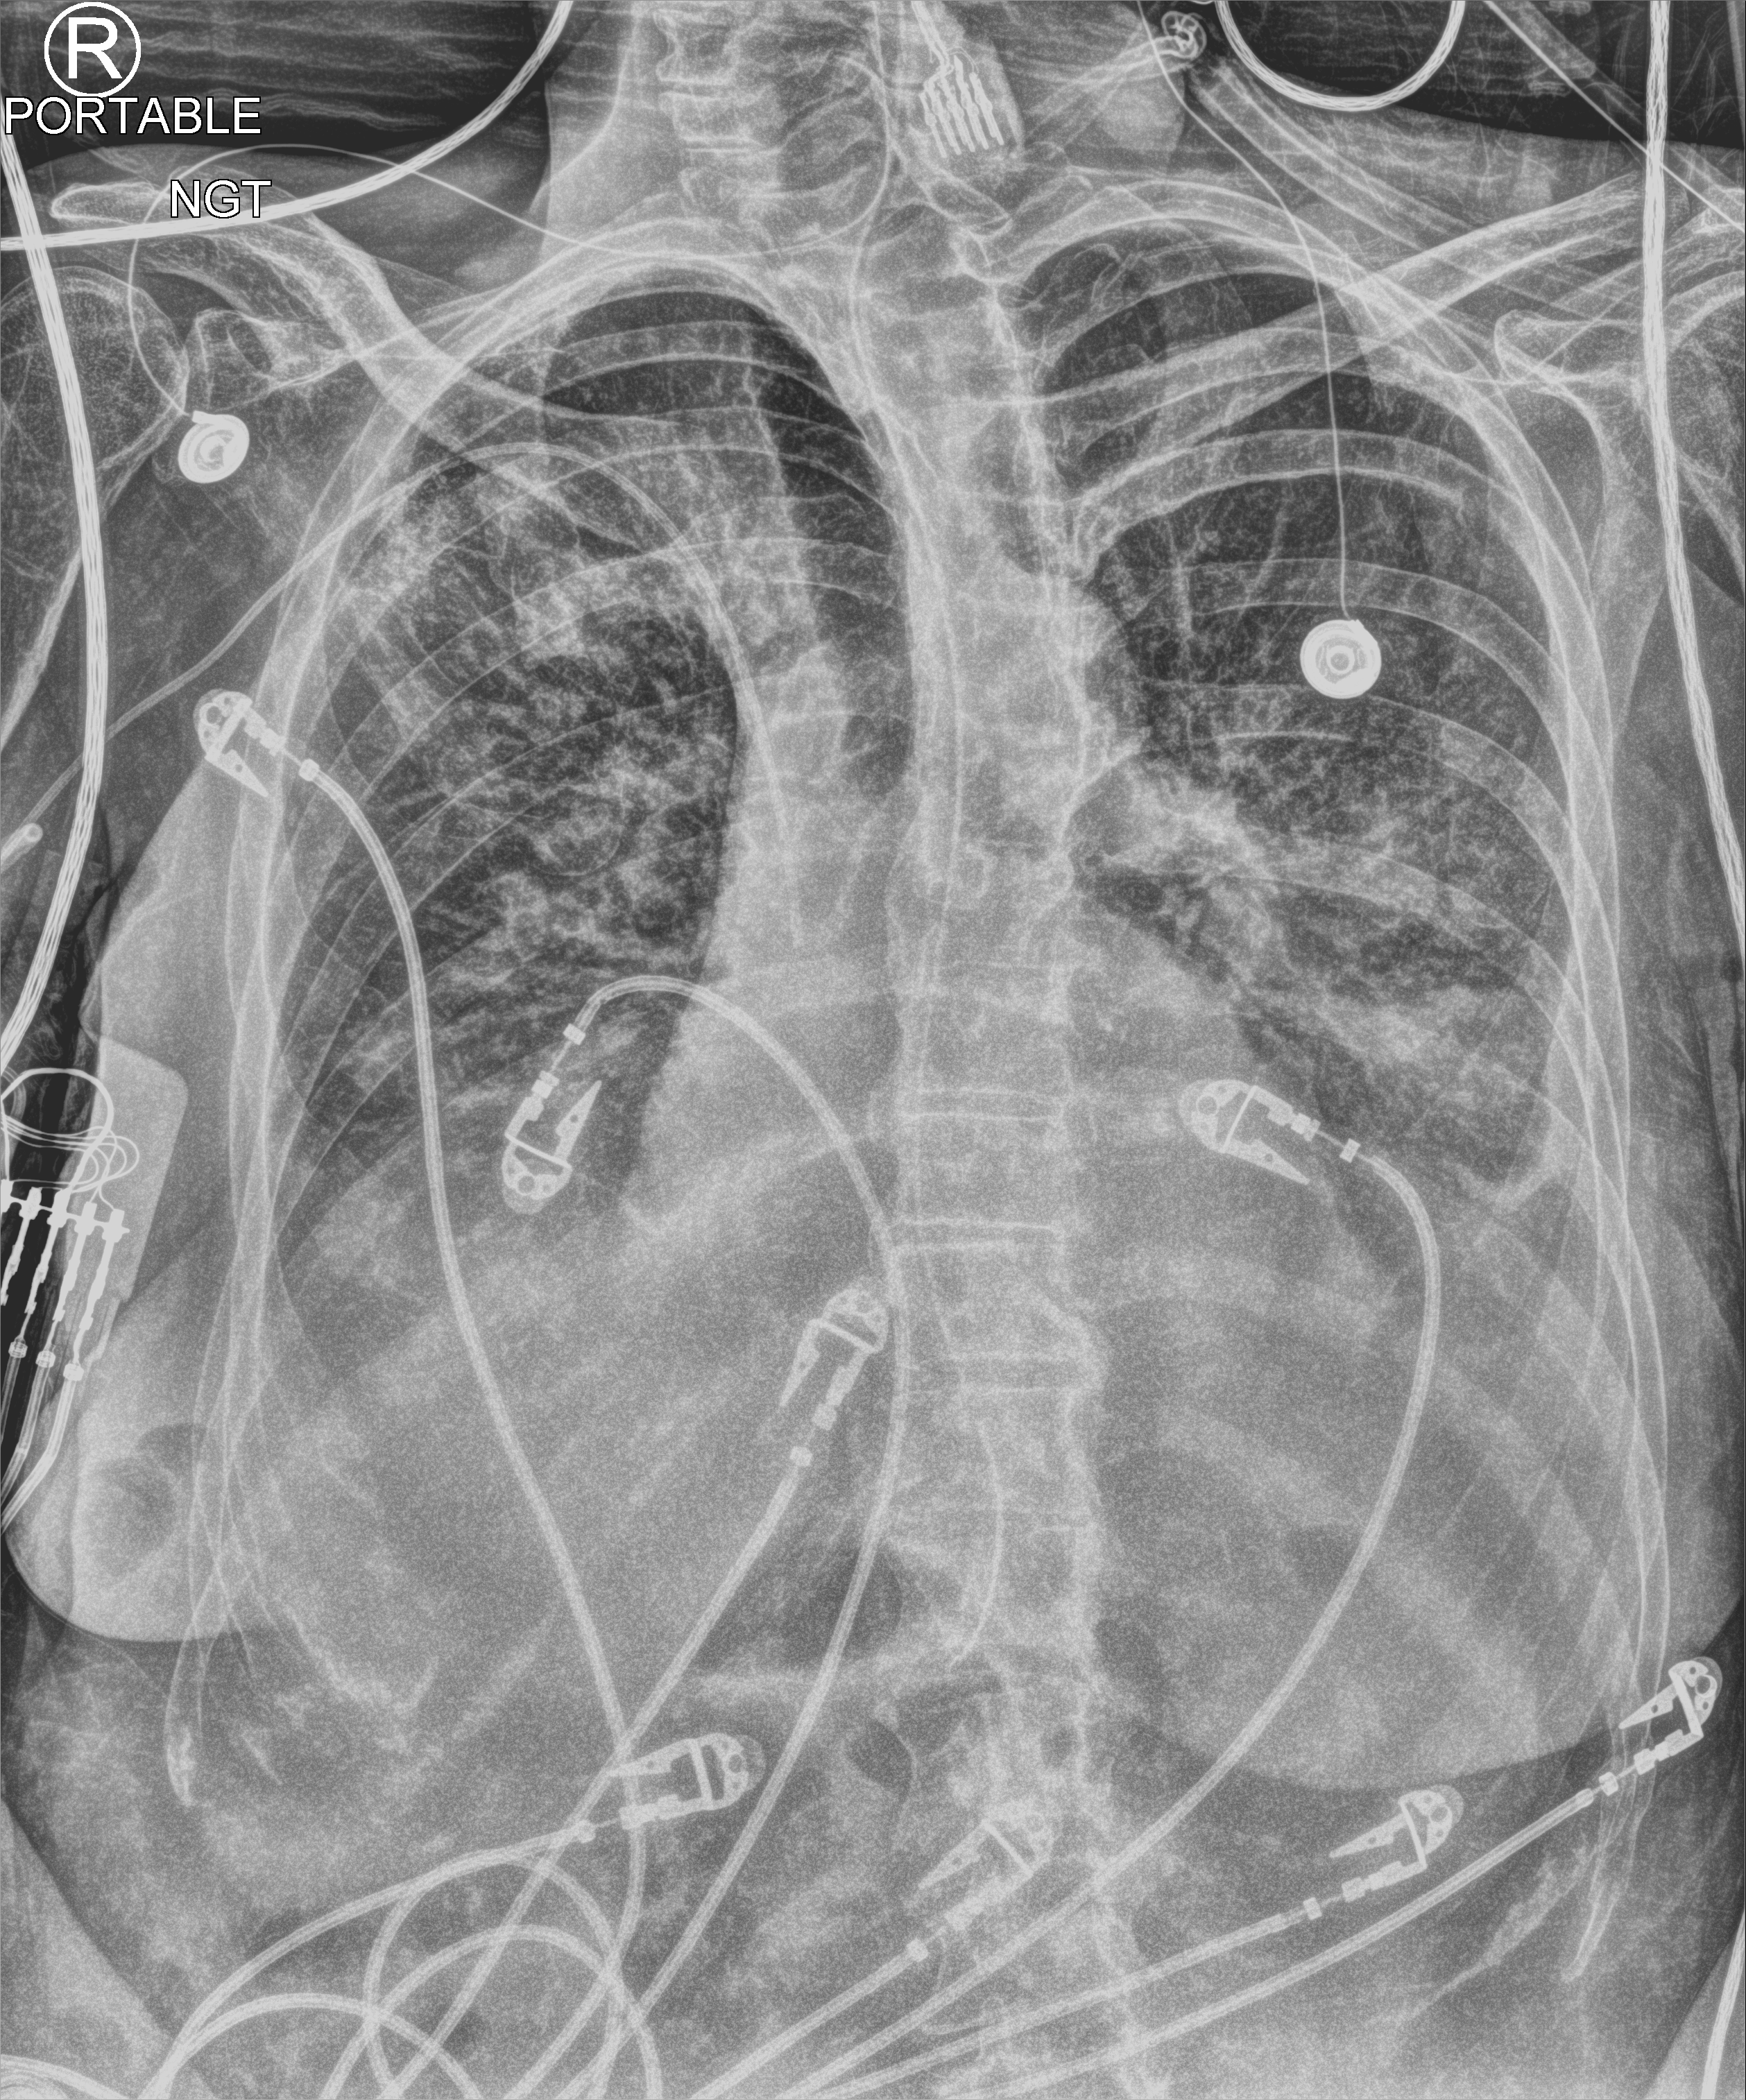
Bedside chest radiograph (computed radiography), anteroposterior (AP) projection. Female patient hospitalised with COVID-19, age 60–74 years.
Admission-level facts for this patient (not findings on this image; timing relative to this image not recorded): mechanically ventilated during this hospital stay: no; admitted to intensive care during this hospital stay: yes.